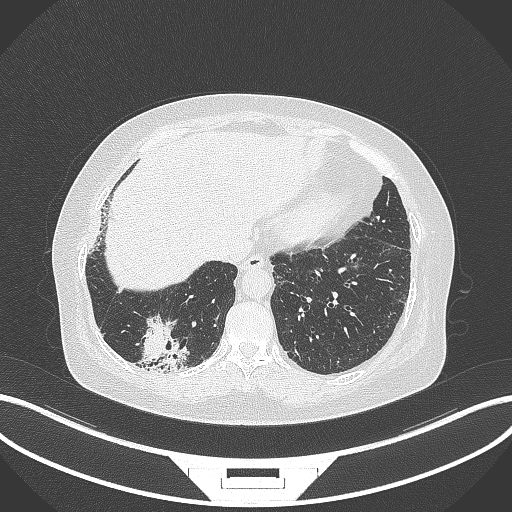
Chest CT, one axial slice. Slice 39 of 296 in the series (ordered by position). Reconstruction kernel B70f. Lung window (W 1500 / L -600 HU). 512 × 512 image matrix, field of view 400 × 400 mm. Female patient, age 65 years. Case-level facts recorded for this patient, not image findings: clinical TNM (as recorded): T2b N1 M0; histopathological grade: G1.
Annotated regions visible in this slice (rectangle marked by the reading radiologist):
- lung tumour (recorded histology: adenocarcinoma): bounding box <131,313,190,374> (left, top, right, bottom; pixels)